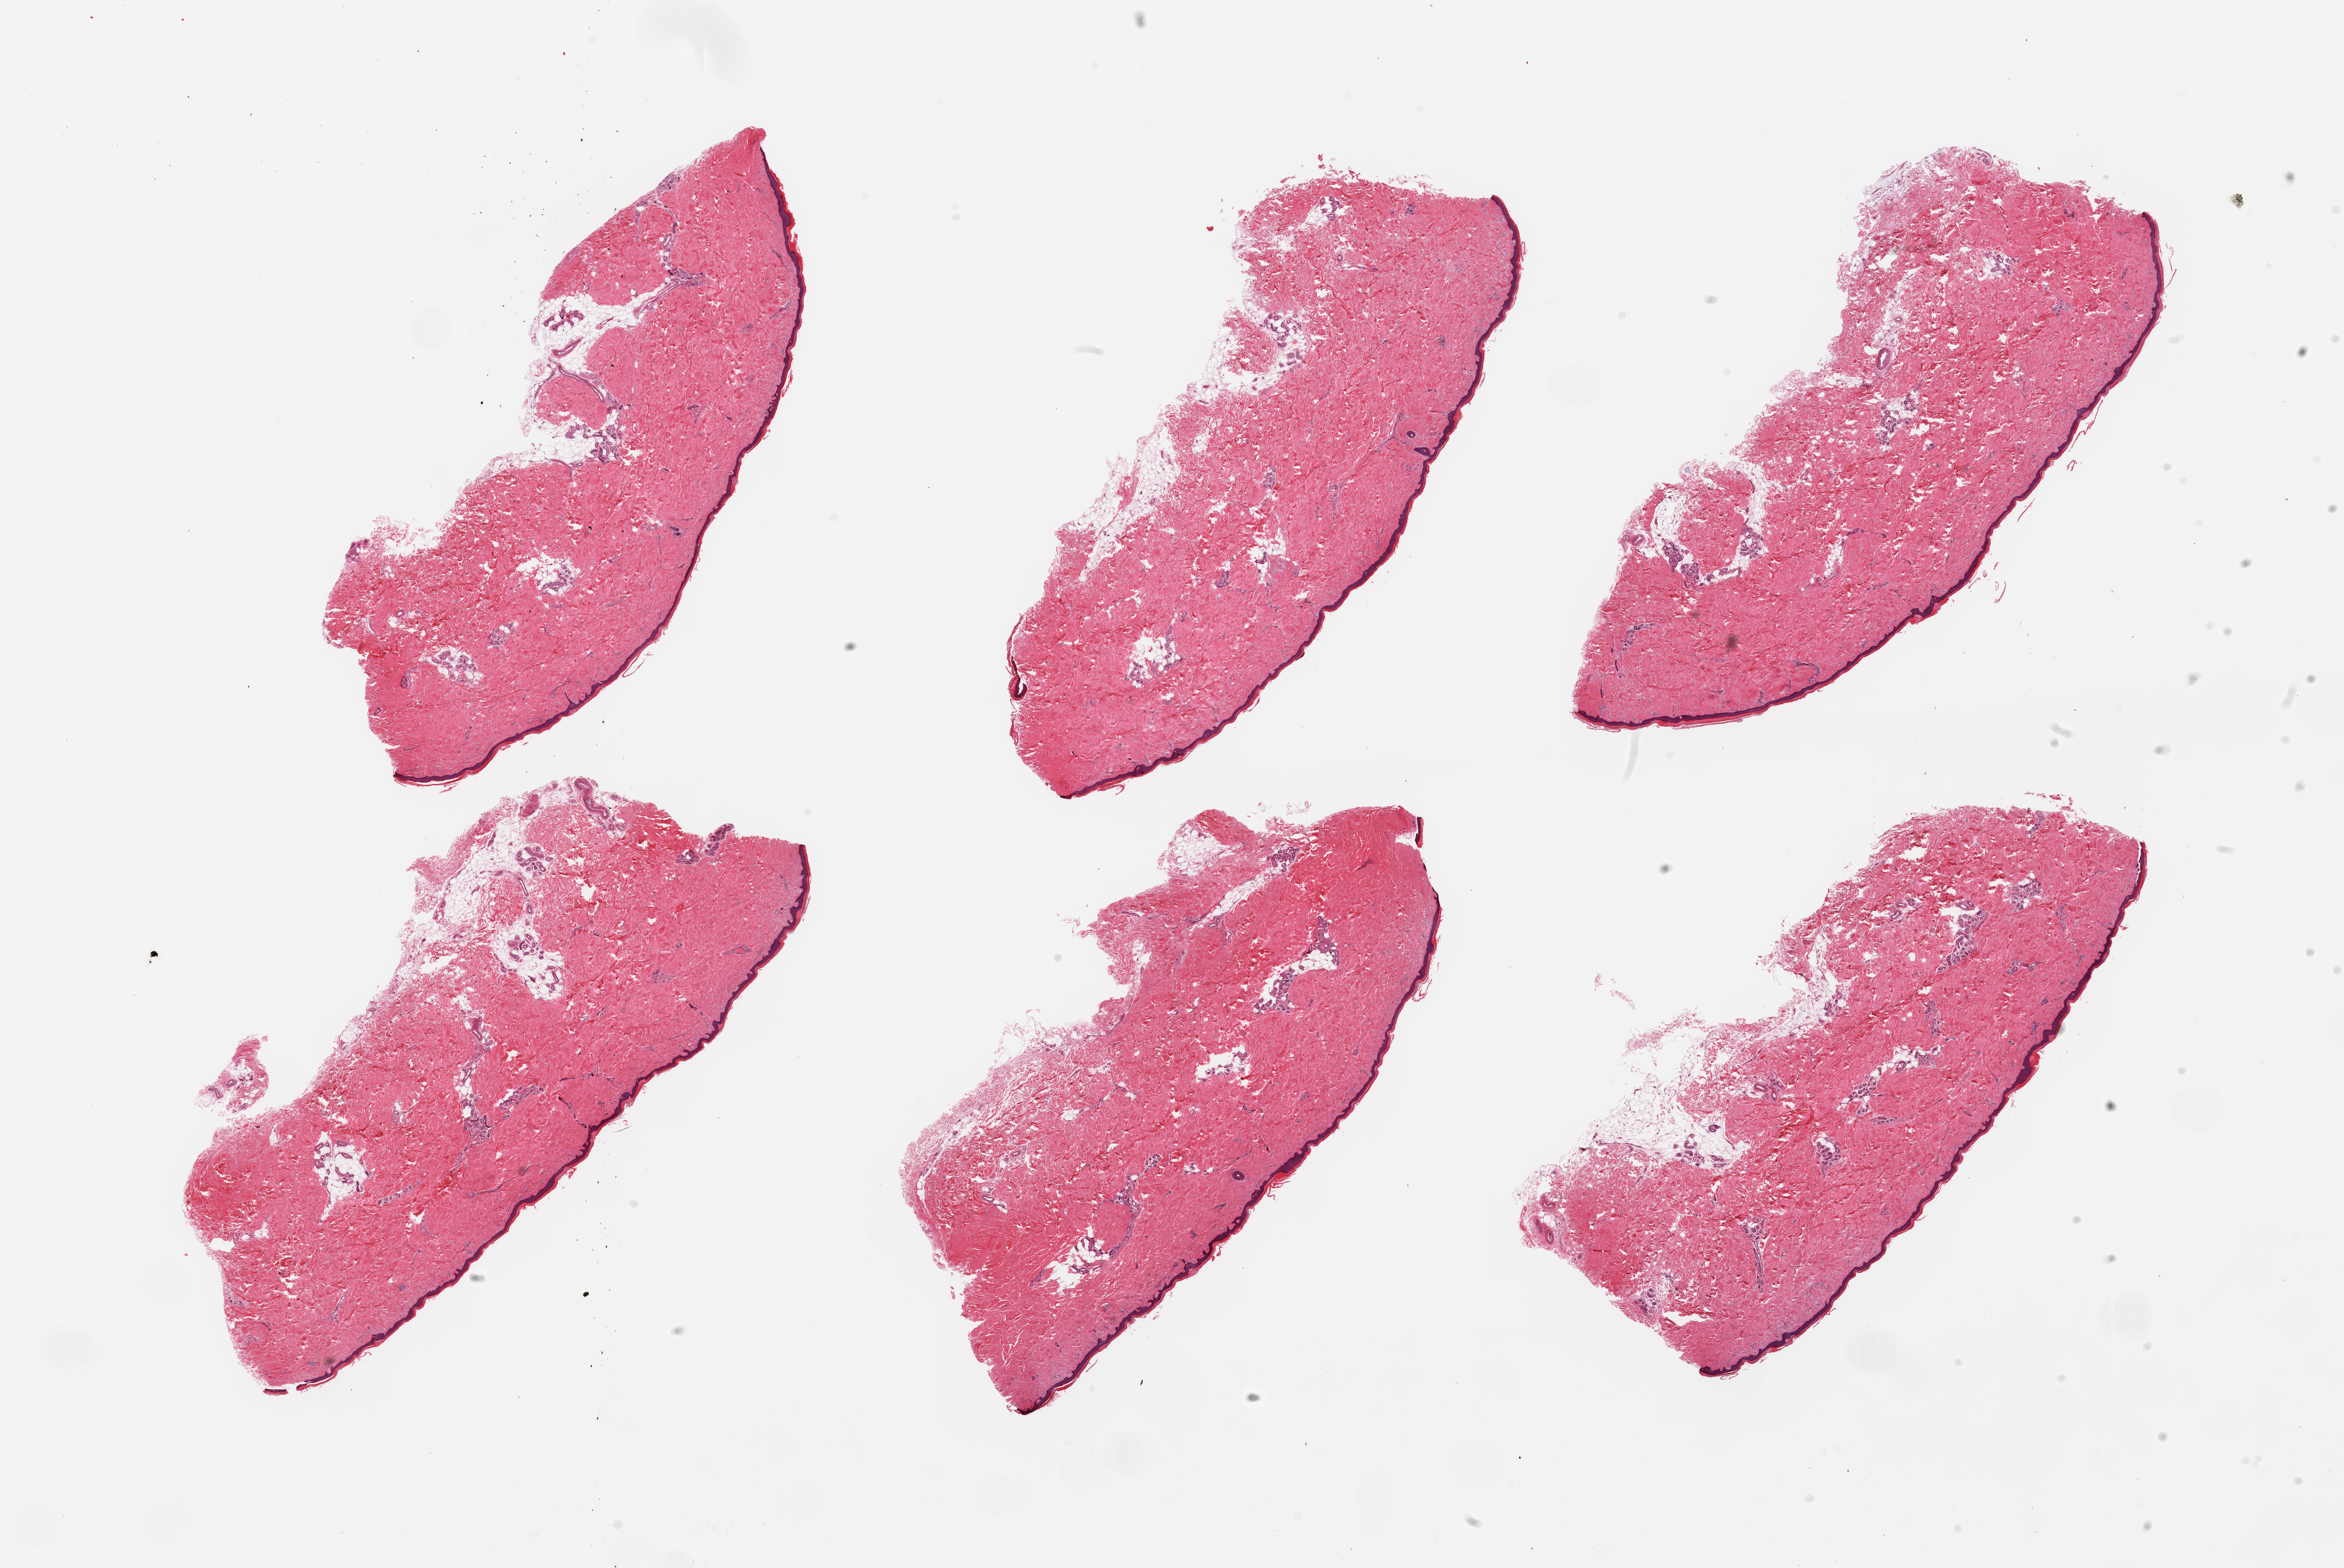
Whole-slide image, hematoxylin and eosin (H&E) stain, a low-resolution overview of the entire scanned area, about 29.5 x 19.8 mm (from a 20x scan); PAXgene-fixed, paraffin-embedded tissue; target tissue: skin of lower leg; tissue donor sample. Donor: male.
* pathologist's review note for this sample: 6 pieces; well trimmed; 10% dermal fat